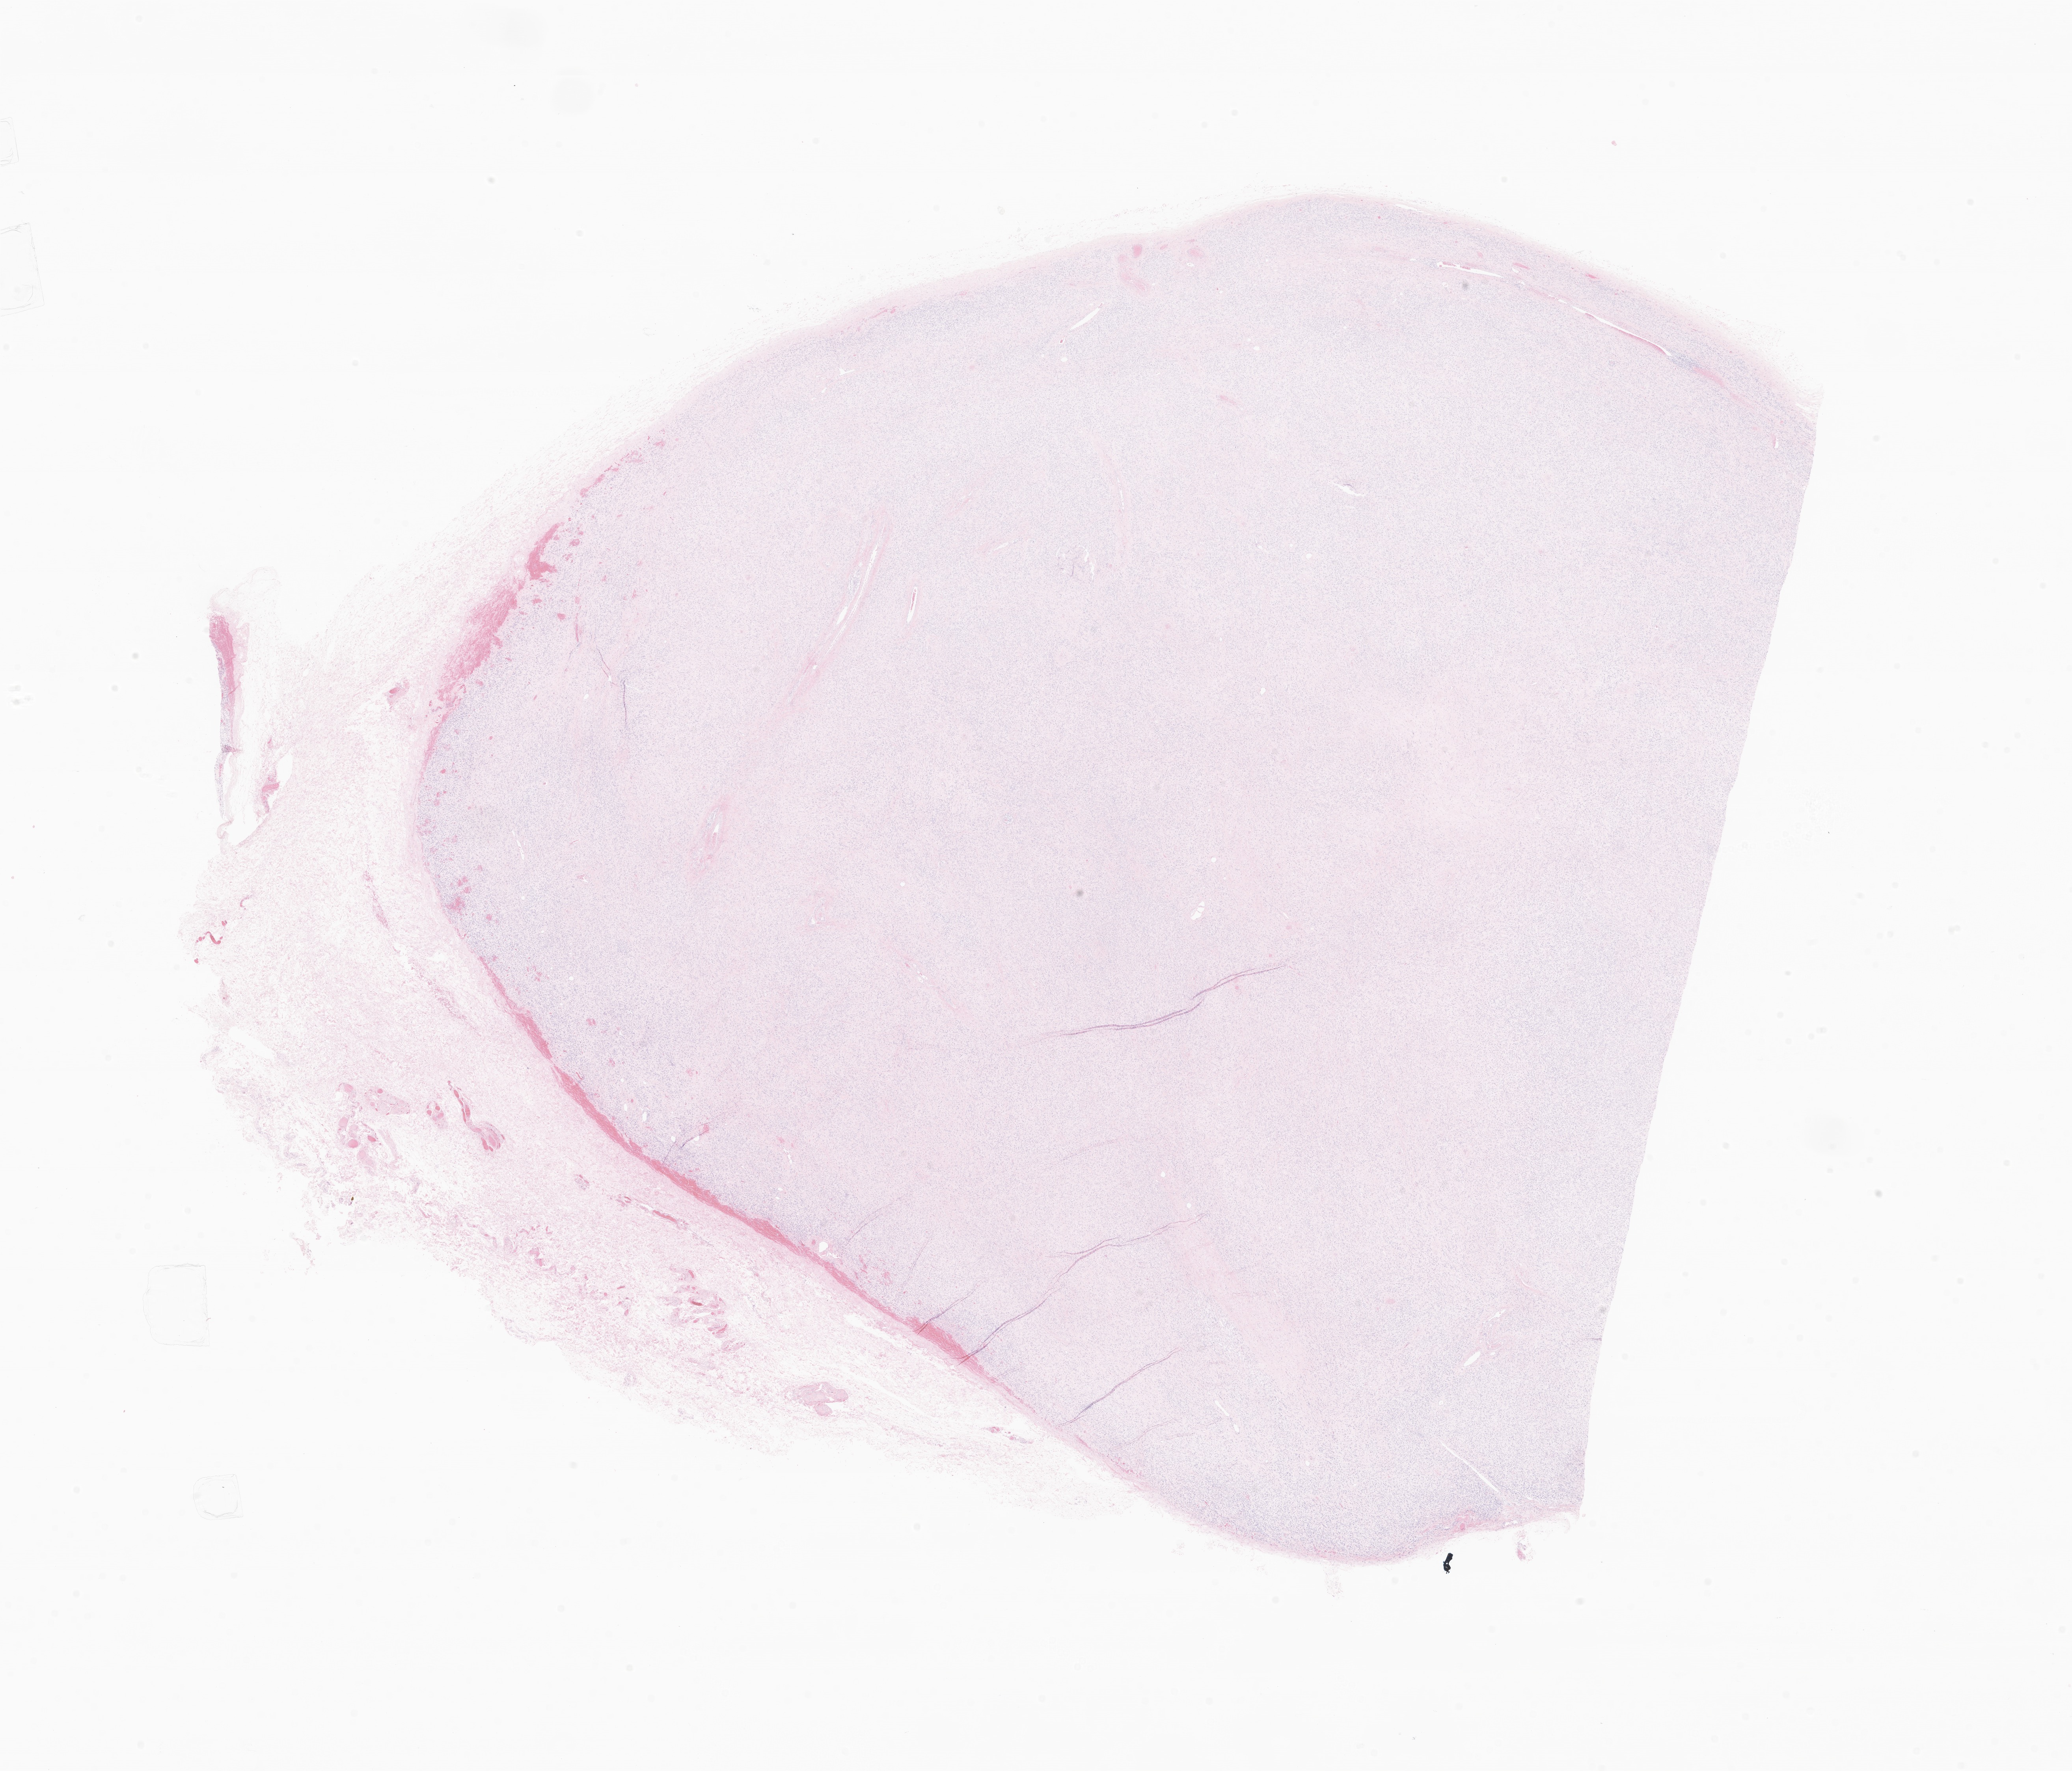
Hematoxylin and eosin (H&E) whole-slide image of tumor tissue from the testis, whole scanned area (about 22.2 x 18.9 mm) shown as a low-resolution overview. Formalin-fixed paraffin-embedded section. Patient male; age 52 months (4 years 4 months).
Recorded diagnosis: Embryonal rhabdomyosarcoma, NOS.